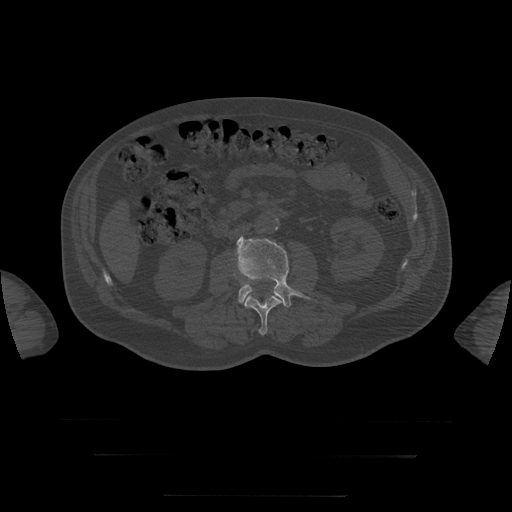
CT including the spine, one axial slice; position 9 of 397 along the scan axis; reconstruction kernel STANDARD; 120 kVp; bone window (W 1800 / L 400 HU); 1.25 mm slice thickness; 512 × 512 image matrix, field of view 510 × 510 mm. Patient age 73 years. Case-level facts recorded for this patient, not image findings: primary cancer: prostate.
Annotated regions visible in this slice (semi-automatically segmented with operator editing):
- L3 vertebra: bounding box <237,237,310,308> (left, top, right, bottom; pixels)